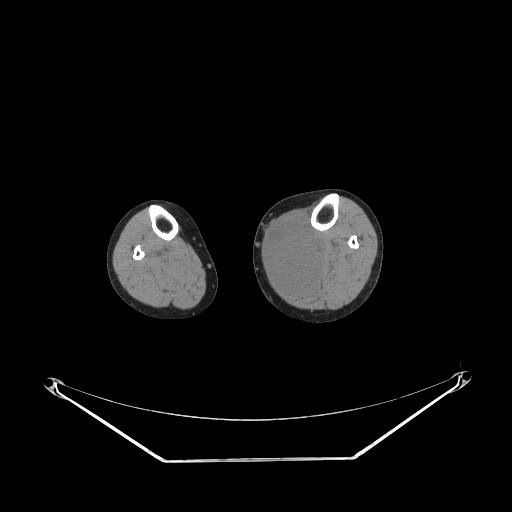
CT of an extremity soft-tissue mass (from a PET/CT study), one axial slice; slice 141 of 223 in the series (ordered by position); reconstruction kernel STANDARD; 140 kVp; soft-tissue window (W 400 / L 40 HU); 3.75 mm slice thickness; 512 × 512 image matrix, field of view 500 × 500 mm. Female patient. From the clinical record (not read from this slice): histological type: extraskeletal high grade osteogenic sarcoma; grade: high; site of the primary tumour: left calf.
Outlined on this slice (expert contour drawn on MRI and transferred to this co-registered scan by the dataset authors):
- gross tumour volume (mass): bounding box [x1, y1, x2, y2] px = [270, 224, 321, 289]